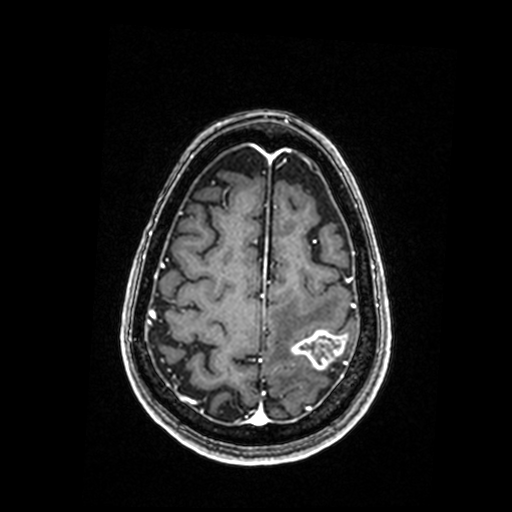
Brain MRI from a brain-tumour surgery series, one axial slice; slice 51 of 192 in the series (ordered by position); T1-weighted post-contrast; 0.98 mm slice thickness; 512 × 512 image matrix, field of view 250 × 250 mm. Case-level facts recorded for this patient, not image findings: histopathology: Metastastic Carcinoma, Poorly Differentiated; tumour location: Left Parietal.
Structures marked on this image (expert manual segmentation):
- tumour: bounding box [x1, y1, x2, y2] px = [292, 330, 347, 370]